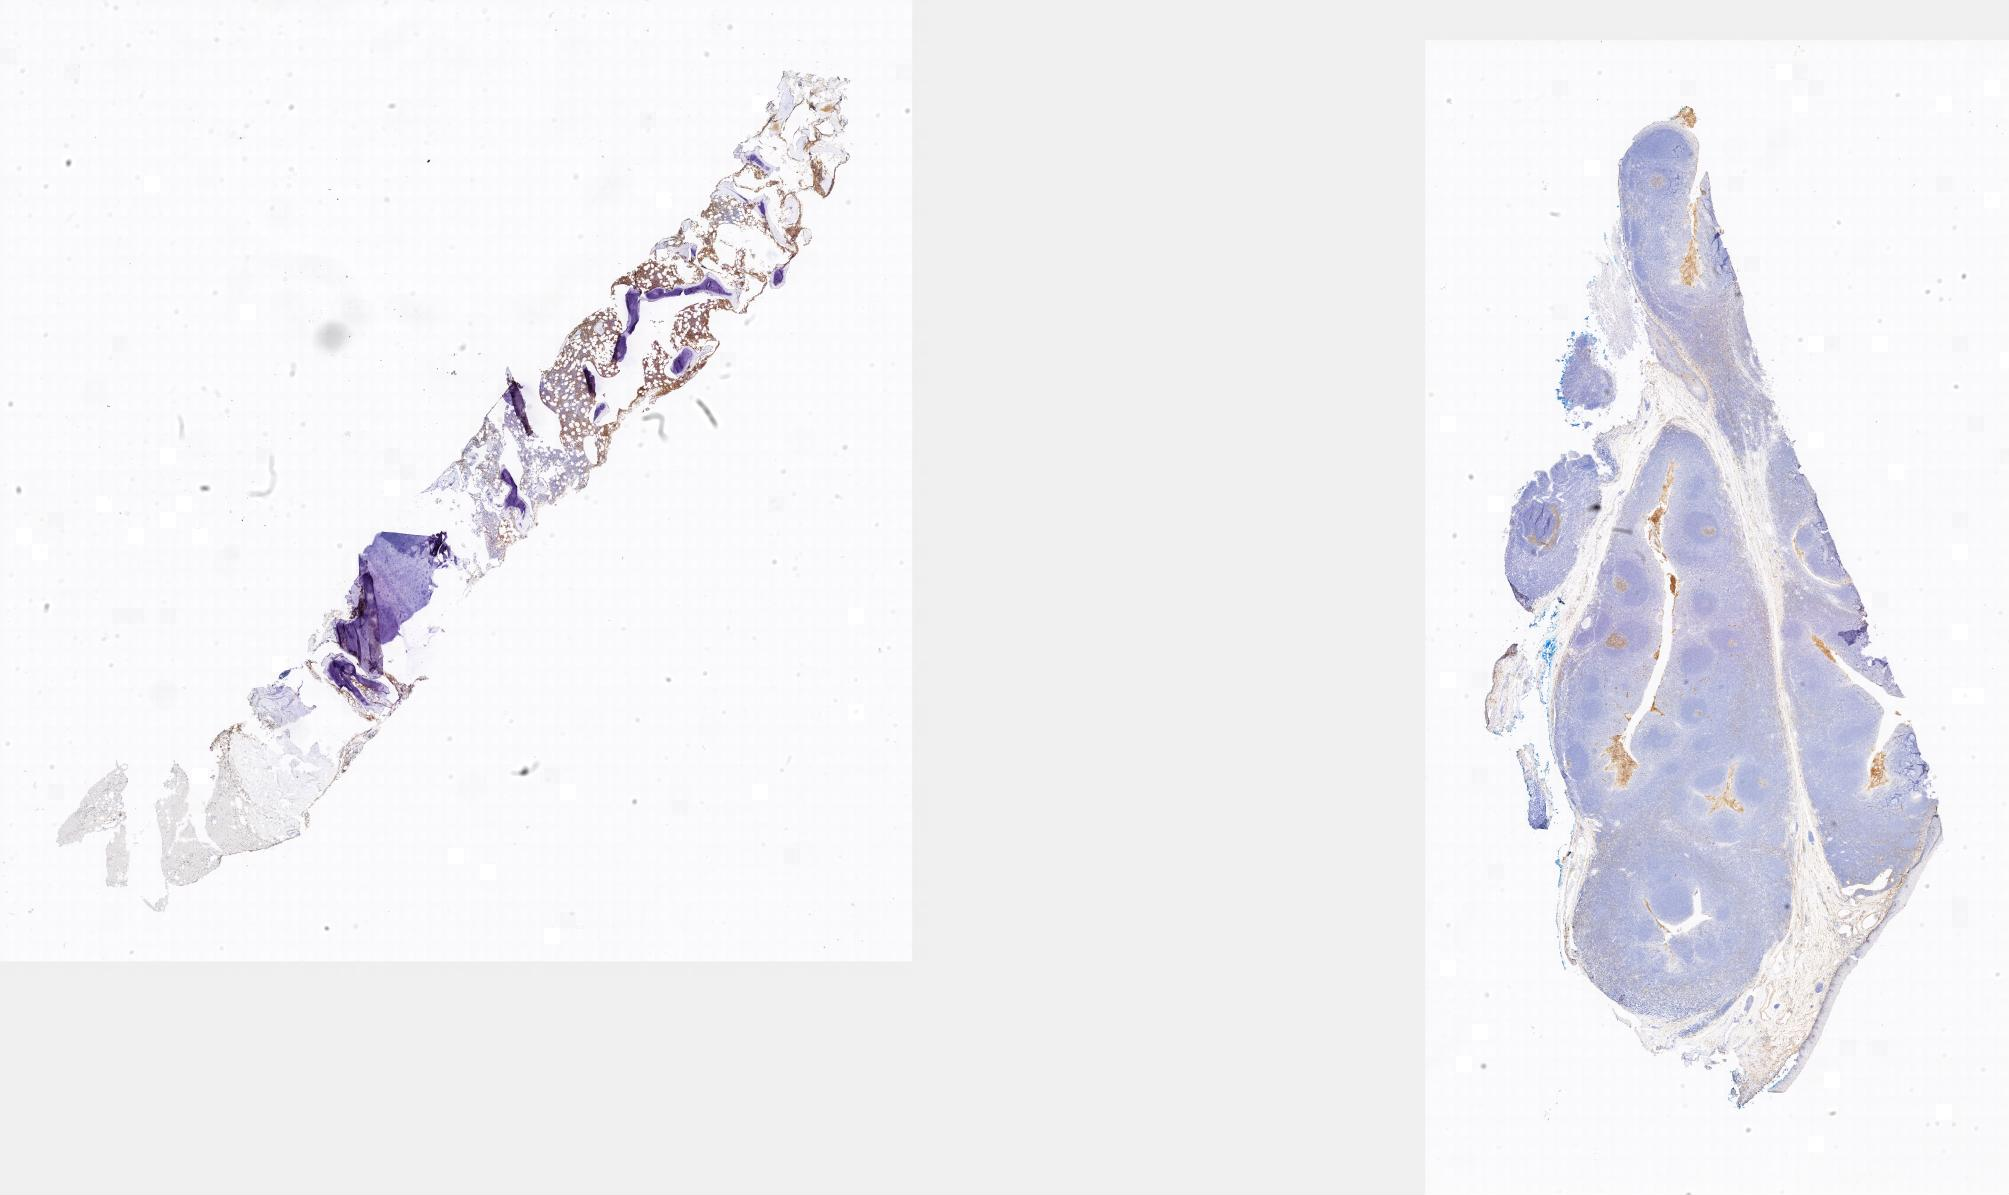
Whole-slide image, immunohistochemical stain for CD10 — low-resolution overview of the scanned area; tumor tissue; anatomic site: bone marrow. Patient male; 15 years old.
Histologic diagnosis: Burkitt lymphoma, NOS.